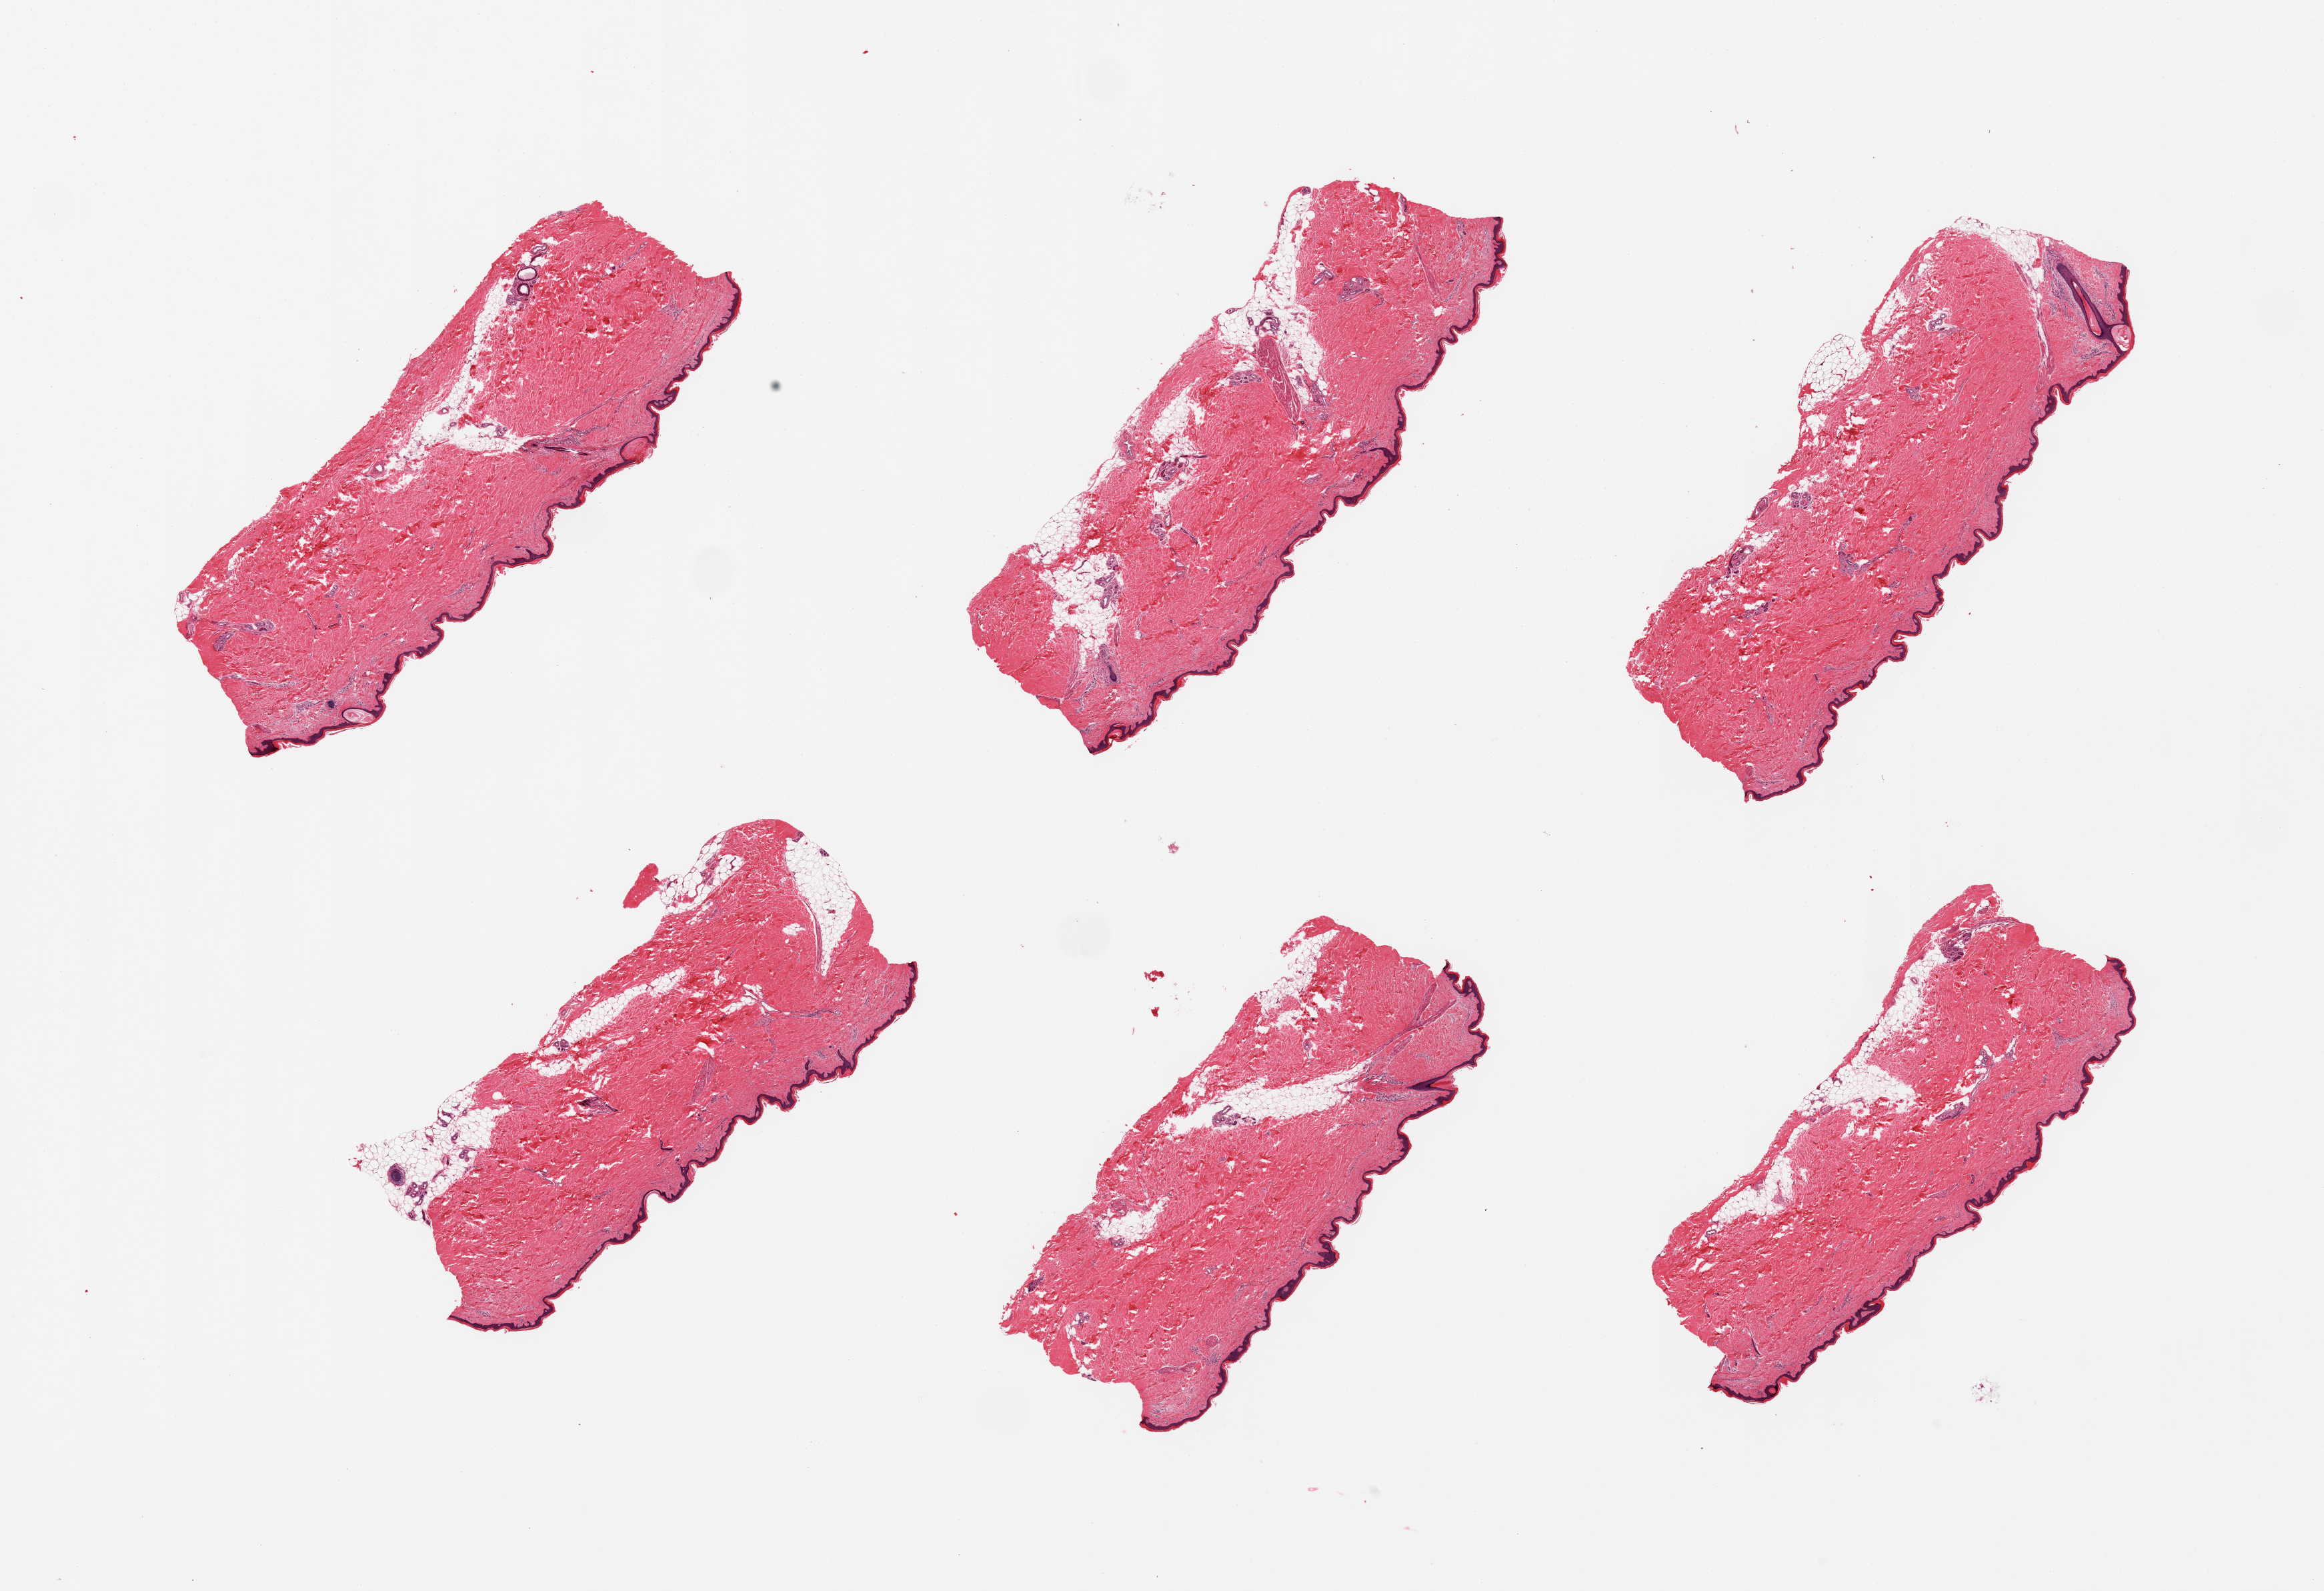
Haematoxylin and eosin whole-slide image, shown as a low-resolution overview of the whole scanned area (about 27.6 x 18.9 mm). PAXgene-fixed paraffin-embedded (PFPE) section. Target tissue: skin of lower leg. Tissue donor sample. Male donor.
Pathologist's review note for this sample: 6 pieces; include 5-10% internal (predominant) and attached fat, epidermis measures about 35 microns.